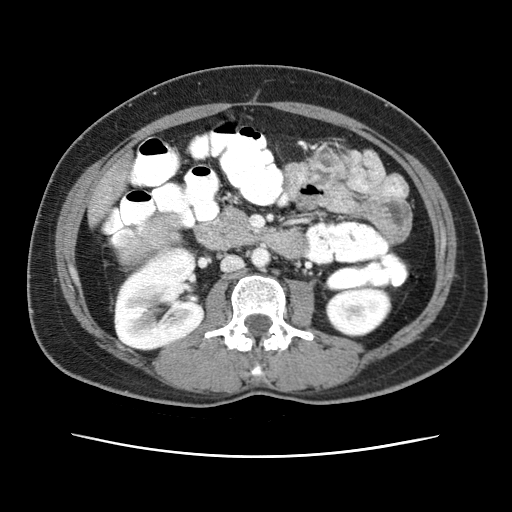
Contrast-enhanced abdominal CT (liver protocol), one axial slice; slice 6 of 79 in the series (ordered by position); reconstruction kernel STANDARD; 120 kVp; soft-tissue window (W 400 / L 40 HU); 512 × 512 image matrix, field of view 340 × 340 mm. Case-level facts recorded for this patient, not image findings: diagnosis: hepatocellular carcinoma (patient treated with transarterial chemoembolisation; whether this scan precedes or follows treatment is not stated here); TNM stage (as recorded): Stage-I; Child-Pugh class: A.
Annotated regions visible in this slice (semi-automatic segmentation, software-assisted and operator-edited):
- abdominal aorta: bounding box [x1, y1, x2, y2] px = [251, 248, 269, 268]
- liver parenchyma outside the tumour (the mass and vessels are separate outlines, so this box may not span the whole liver): [88, 162, 127, 223]
- mass: [128, 220, 175, 258]